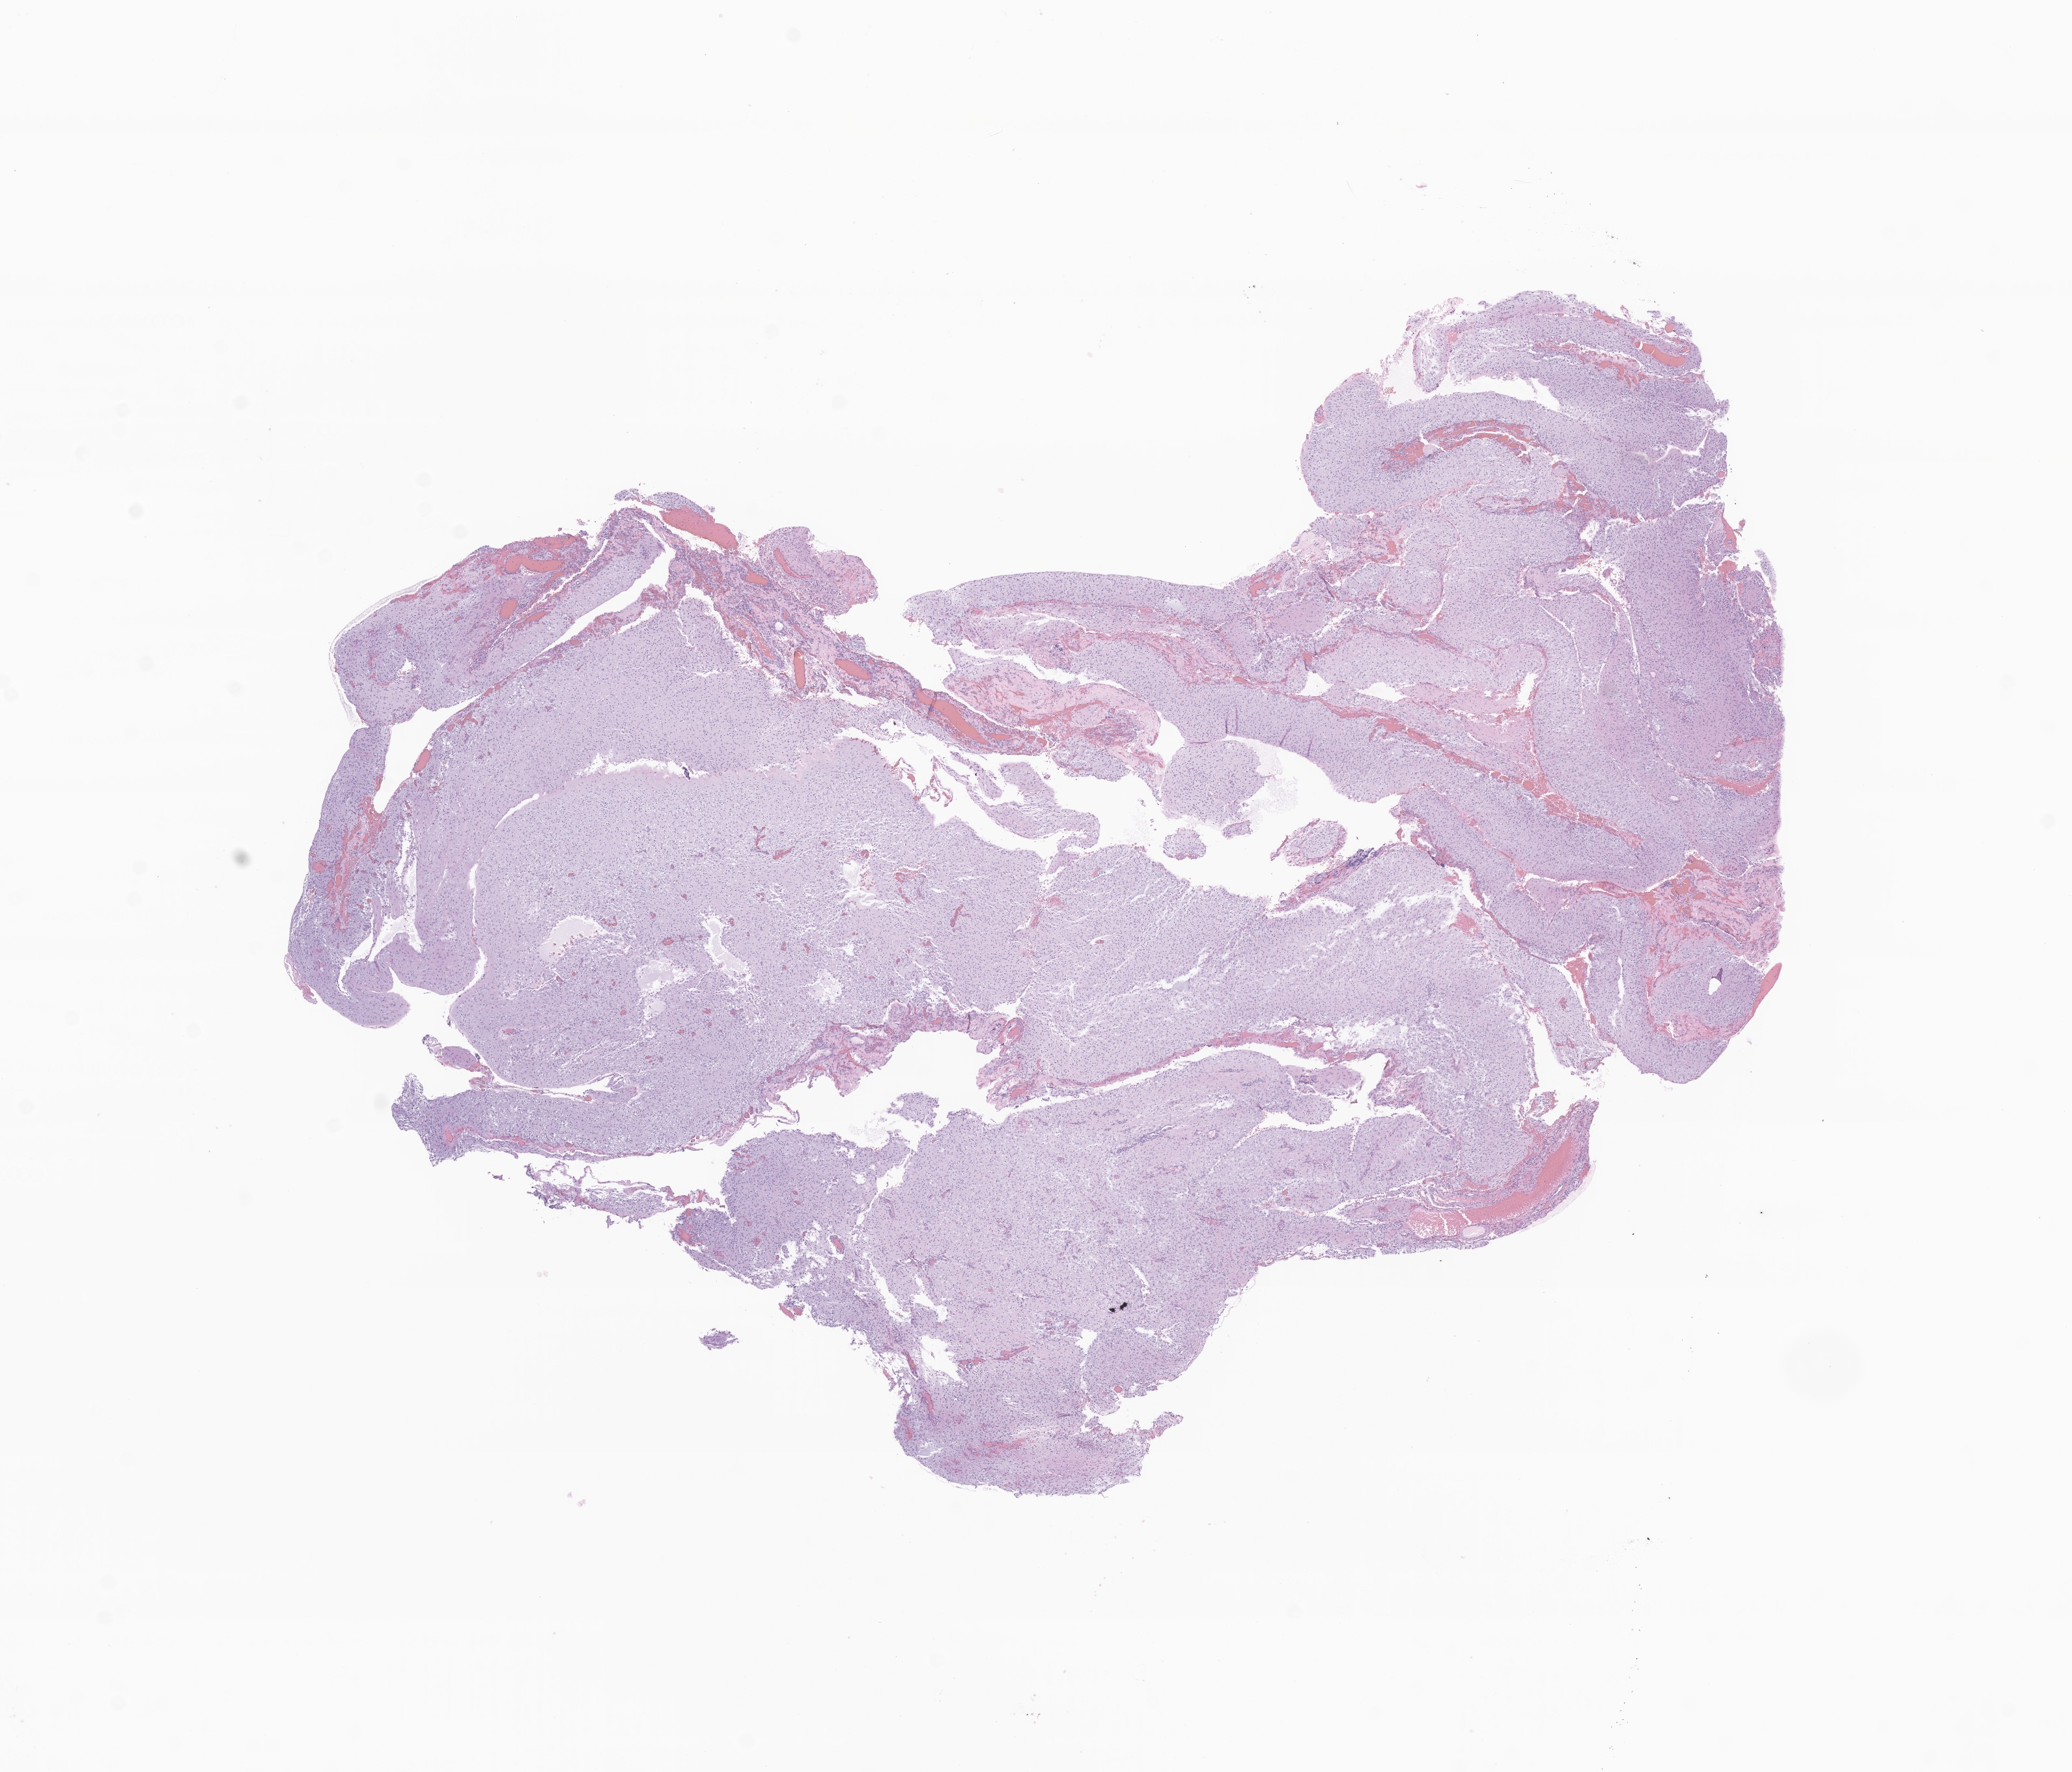
Haematoxylin and eosin whole-slide image of tumor tissue from the brain — shown as a low-resolution overview of the whole scanned area (about 13.4 x 11.5 mm); formalin-fixed, paraffin-embedded (FFPE) tissue. Patient female; age 35 months.
* diagnosis: Medulloblastoma, NOS